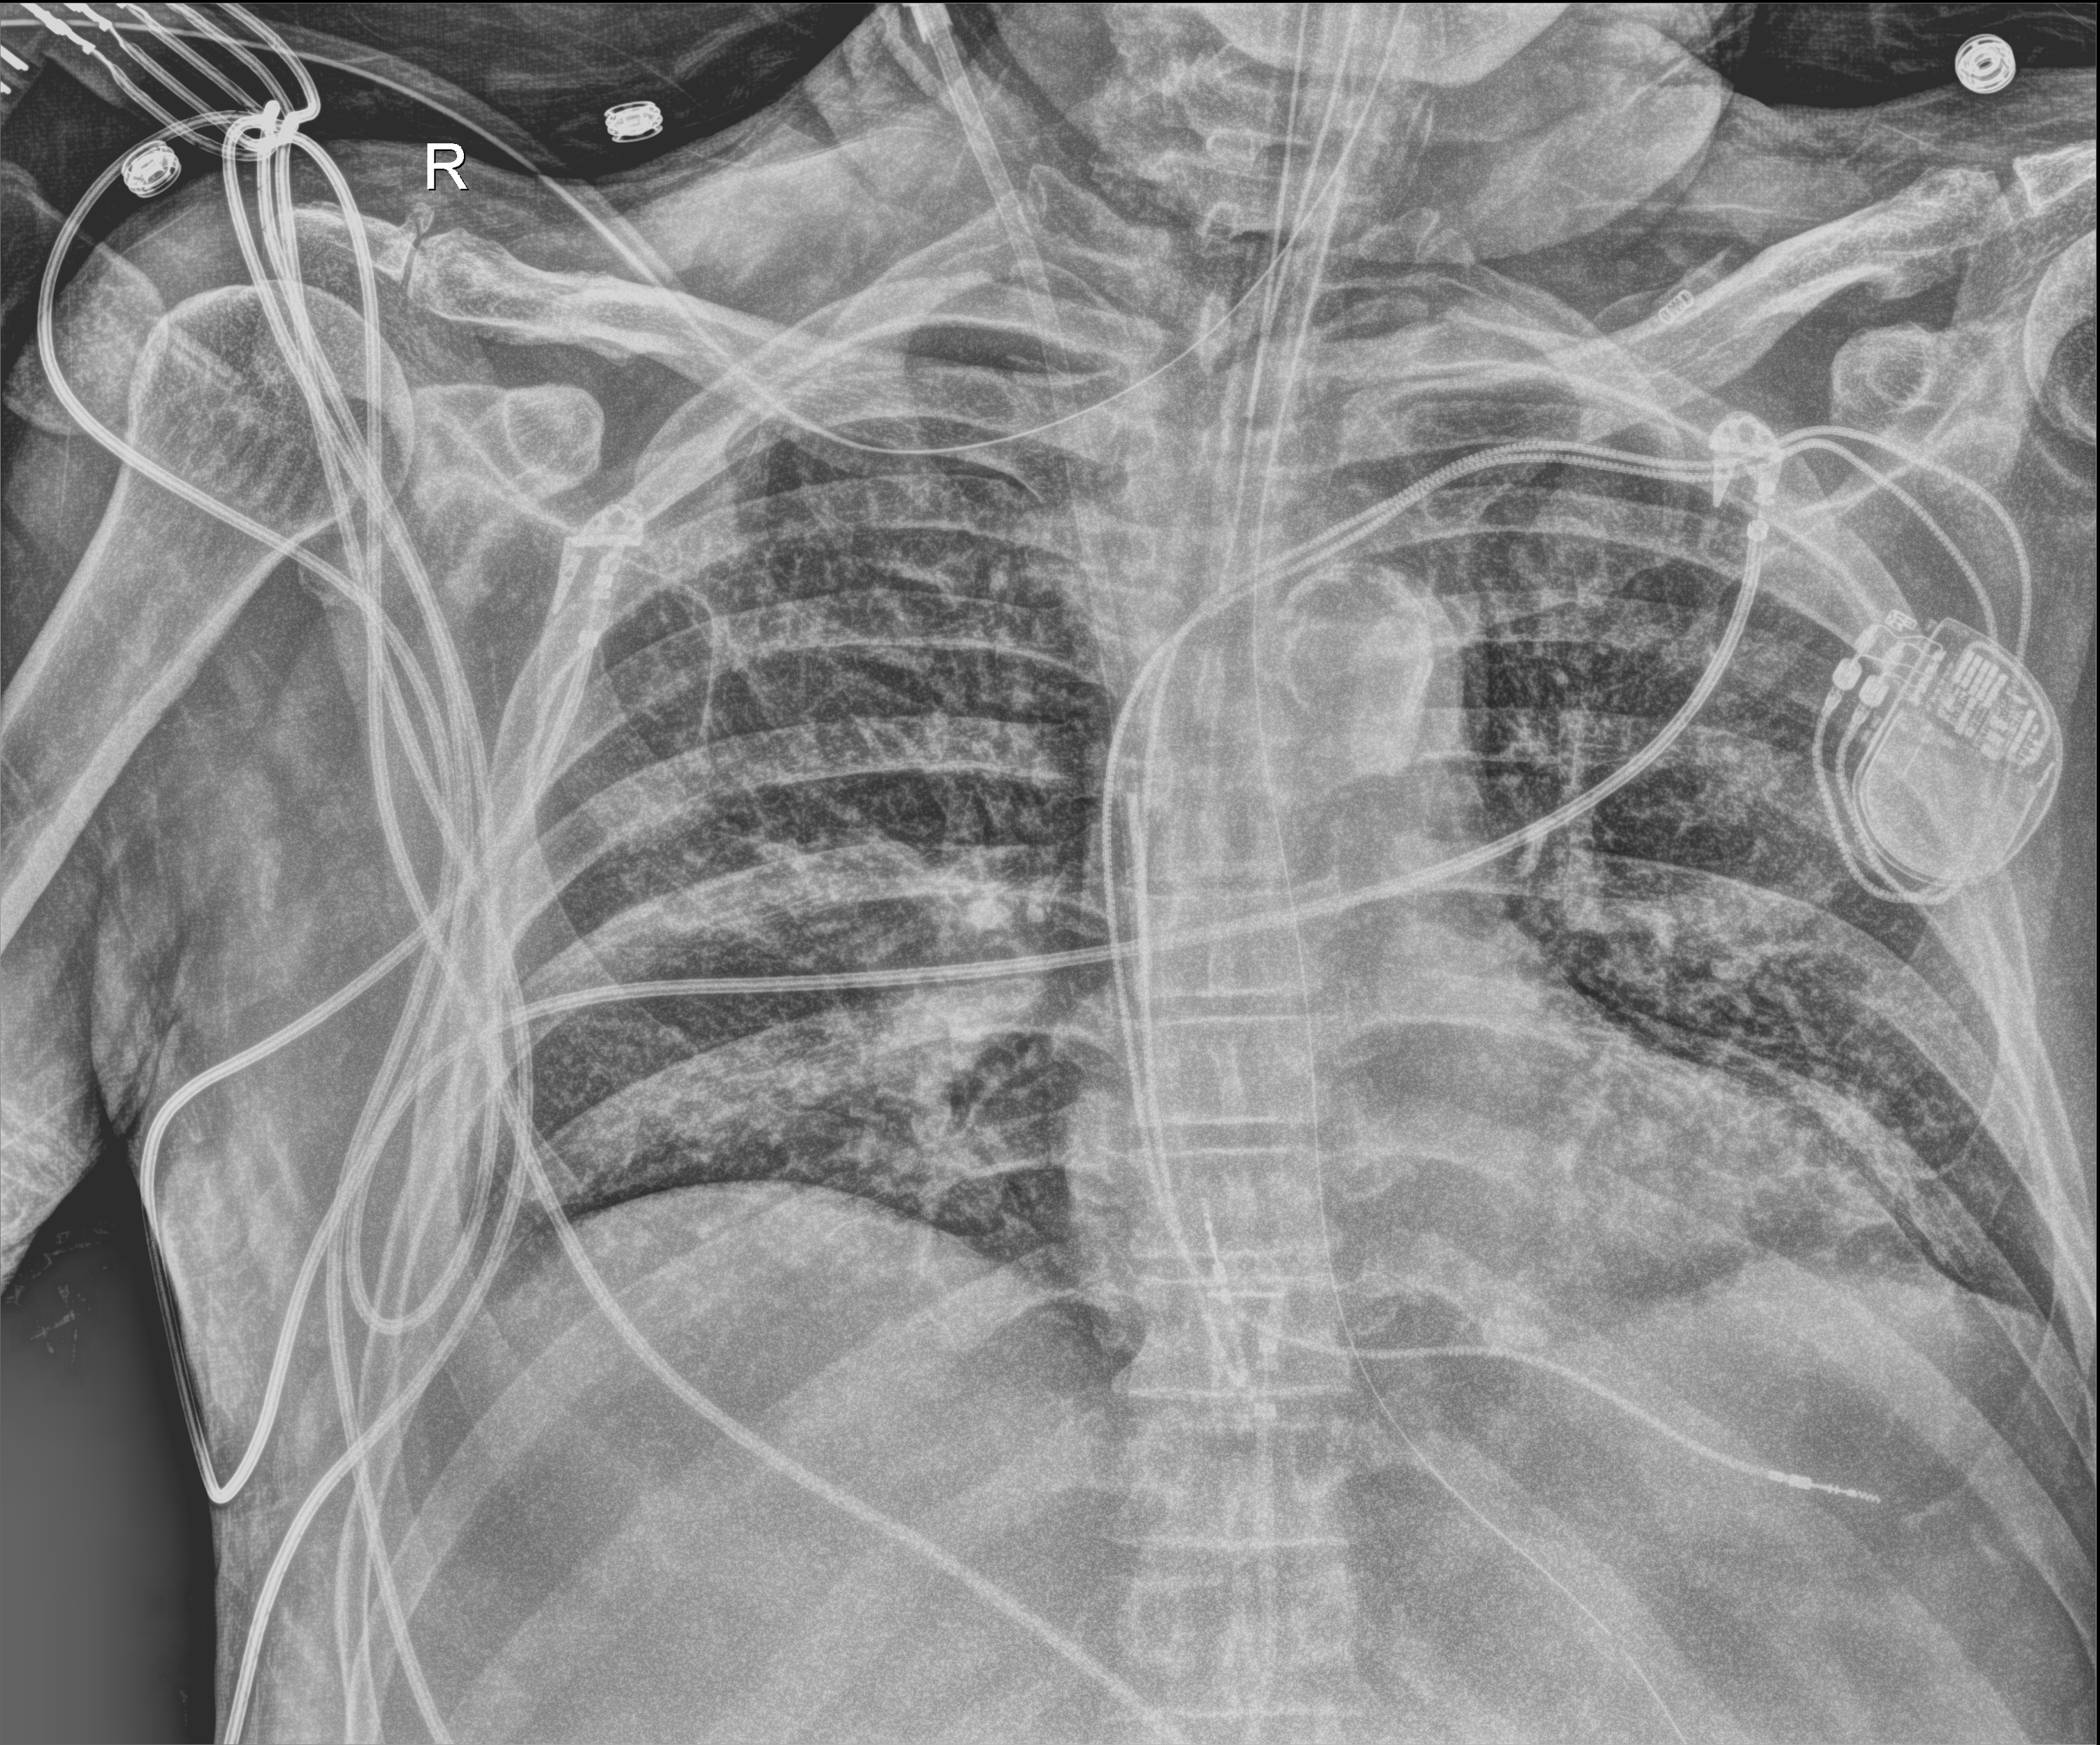
Portable chest radiograph, anteroposterior (AP) projection. Male patient hospitalised with COVID-19, age 60–74 years.
Hospital-stay facts (about this admission, not read from this image; timing relative to this image not recorded): admitted to intensive care during this hospital stay: yes; mechanically ventilated during this hospital stay: yes.